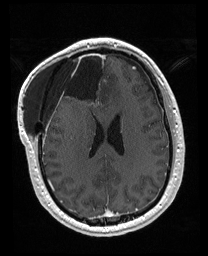
Brain MRI from a brain-tumour surgery series, one axial slice. Position 72 of 176 along the scan axis. T1-weighted post-contrast. 208 × 256 image matrix, field of view 208 × 256 mm. From the clinical record (not read from this slice): histopathology: Astrocytoma; WHO grade: 4; IDH mutation: yes; tumour location: Right Orbitofrontal Anterior Temporal Insular.
Annotated regions visible in this slice (manually delineated by an expert):
- previous resection cavity: box from (x=56, y=52) to (x=106, y=111) px